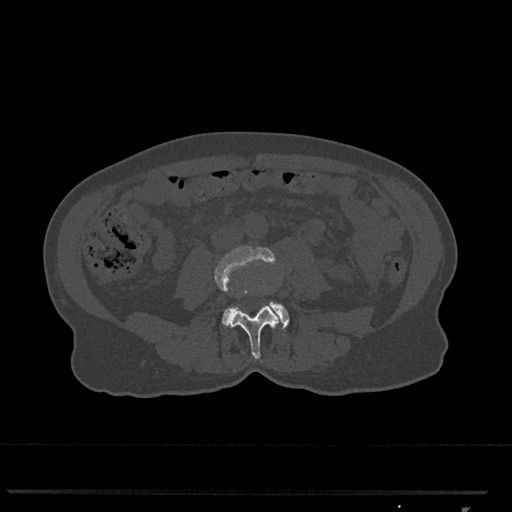
CT including the spine, one axial slice; slice 248 of 793 in the series (ordered by position); reconstruction kernel Br40s/3; 120 kVp; bone window (W 1800 / L 400 HU); 0.5 mm slice thickness; 512 × 512 image matrix, field of view 380 × 380 mm. Patient: female, 62 years. From the clinical record (not read from this slice): primary cancer: renal.
Annotated regions visible in this slice (semi-automatic segmentation, software-assisted and operator-edited):
- L3 vertebra: bounding box (x1, y1, x2, y2) in pixels: (215, 246, 282, 359)
- L4 vertebra: (222, 301, 289, 329)